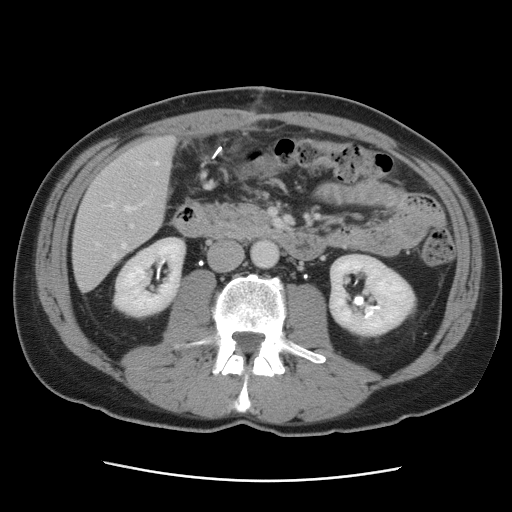
Contrast-enhanced abdominal CT, one axial slice; slice 28 of 89 in the series (ordered by position); intravenous contrast given; soft-tissue window (W 400 / L 40 HU); 5 mm slice thickness; 512 × 512 image matrix, field of view 366 × 366 mm. Male patient, age 59 years. From the clinical record (not read from this slice): diagnosis: colorectal cancer liver metastases, imaged before liver resection; multiple liver metastases: yes; largest metastasis: 0.6 cm; disease in both lobes: yes.
Annotated regions visible in this slice (expert manual segmentation):
- hepatic veins: bounding box [x1, y1, x2, y2] px = [97, 162, 159, 259]
- liver: [74, 139, 174, 290]
- planned liver remnant (the part of the liver to remain after resection): [74, 139, 175, 246]
- portal vein (with intrahepatic branches): [130, 224, 134, 228]